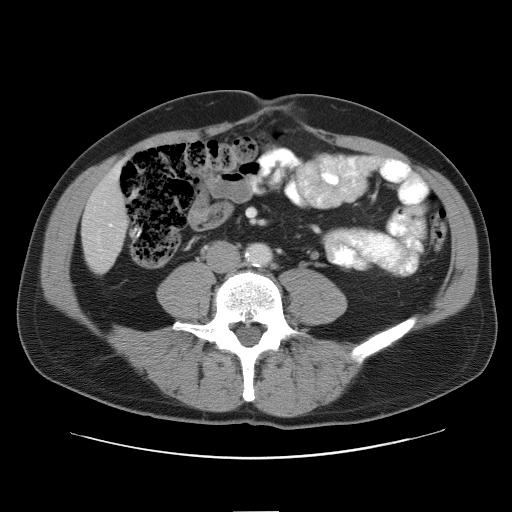
Contrast-enhanced abdominal CT, one axial slice. Position 13 of 52 along the scan axis. Reconstruction kernel STANDARD. Intravenous contrast given. Soft-tissue window (W 400 / L 40 HU). 5 mm slice thickness. 512 × 512 image matrix. Male patient, age 70 years. Case-level facts recorded for this patient, not image findings: diagnosis: colorectal cancer liver metastases, imaged before liver resection.
Outlined on this slice (manually delineated by an expert):
- liver: bounding box (x1, y1, x2, y2) in pixels: (83, 169, 128, 272)
- portal vein (with intrahepatic branches): (109, 224, 113, 226)